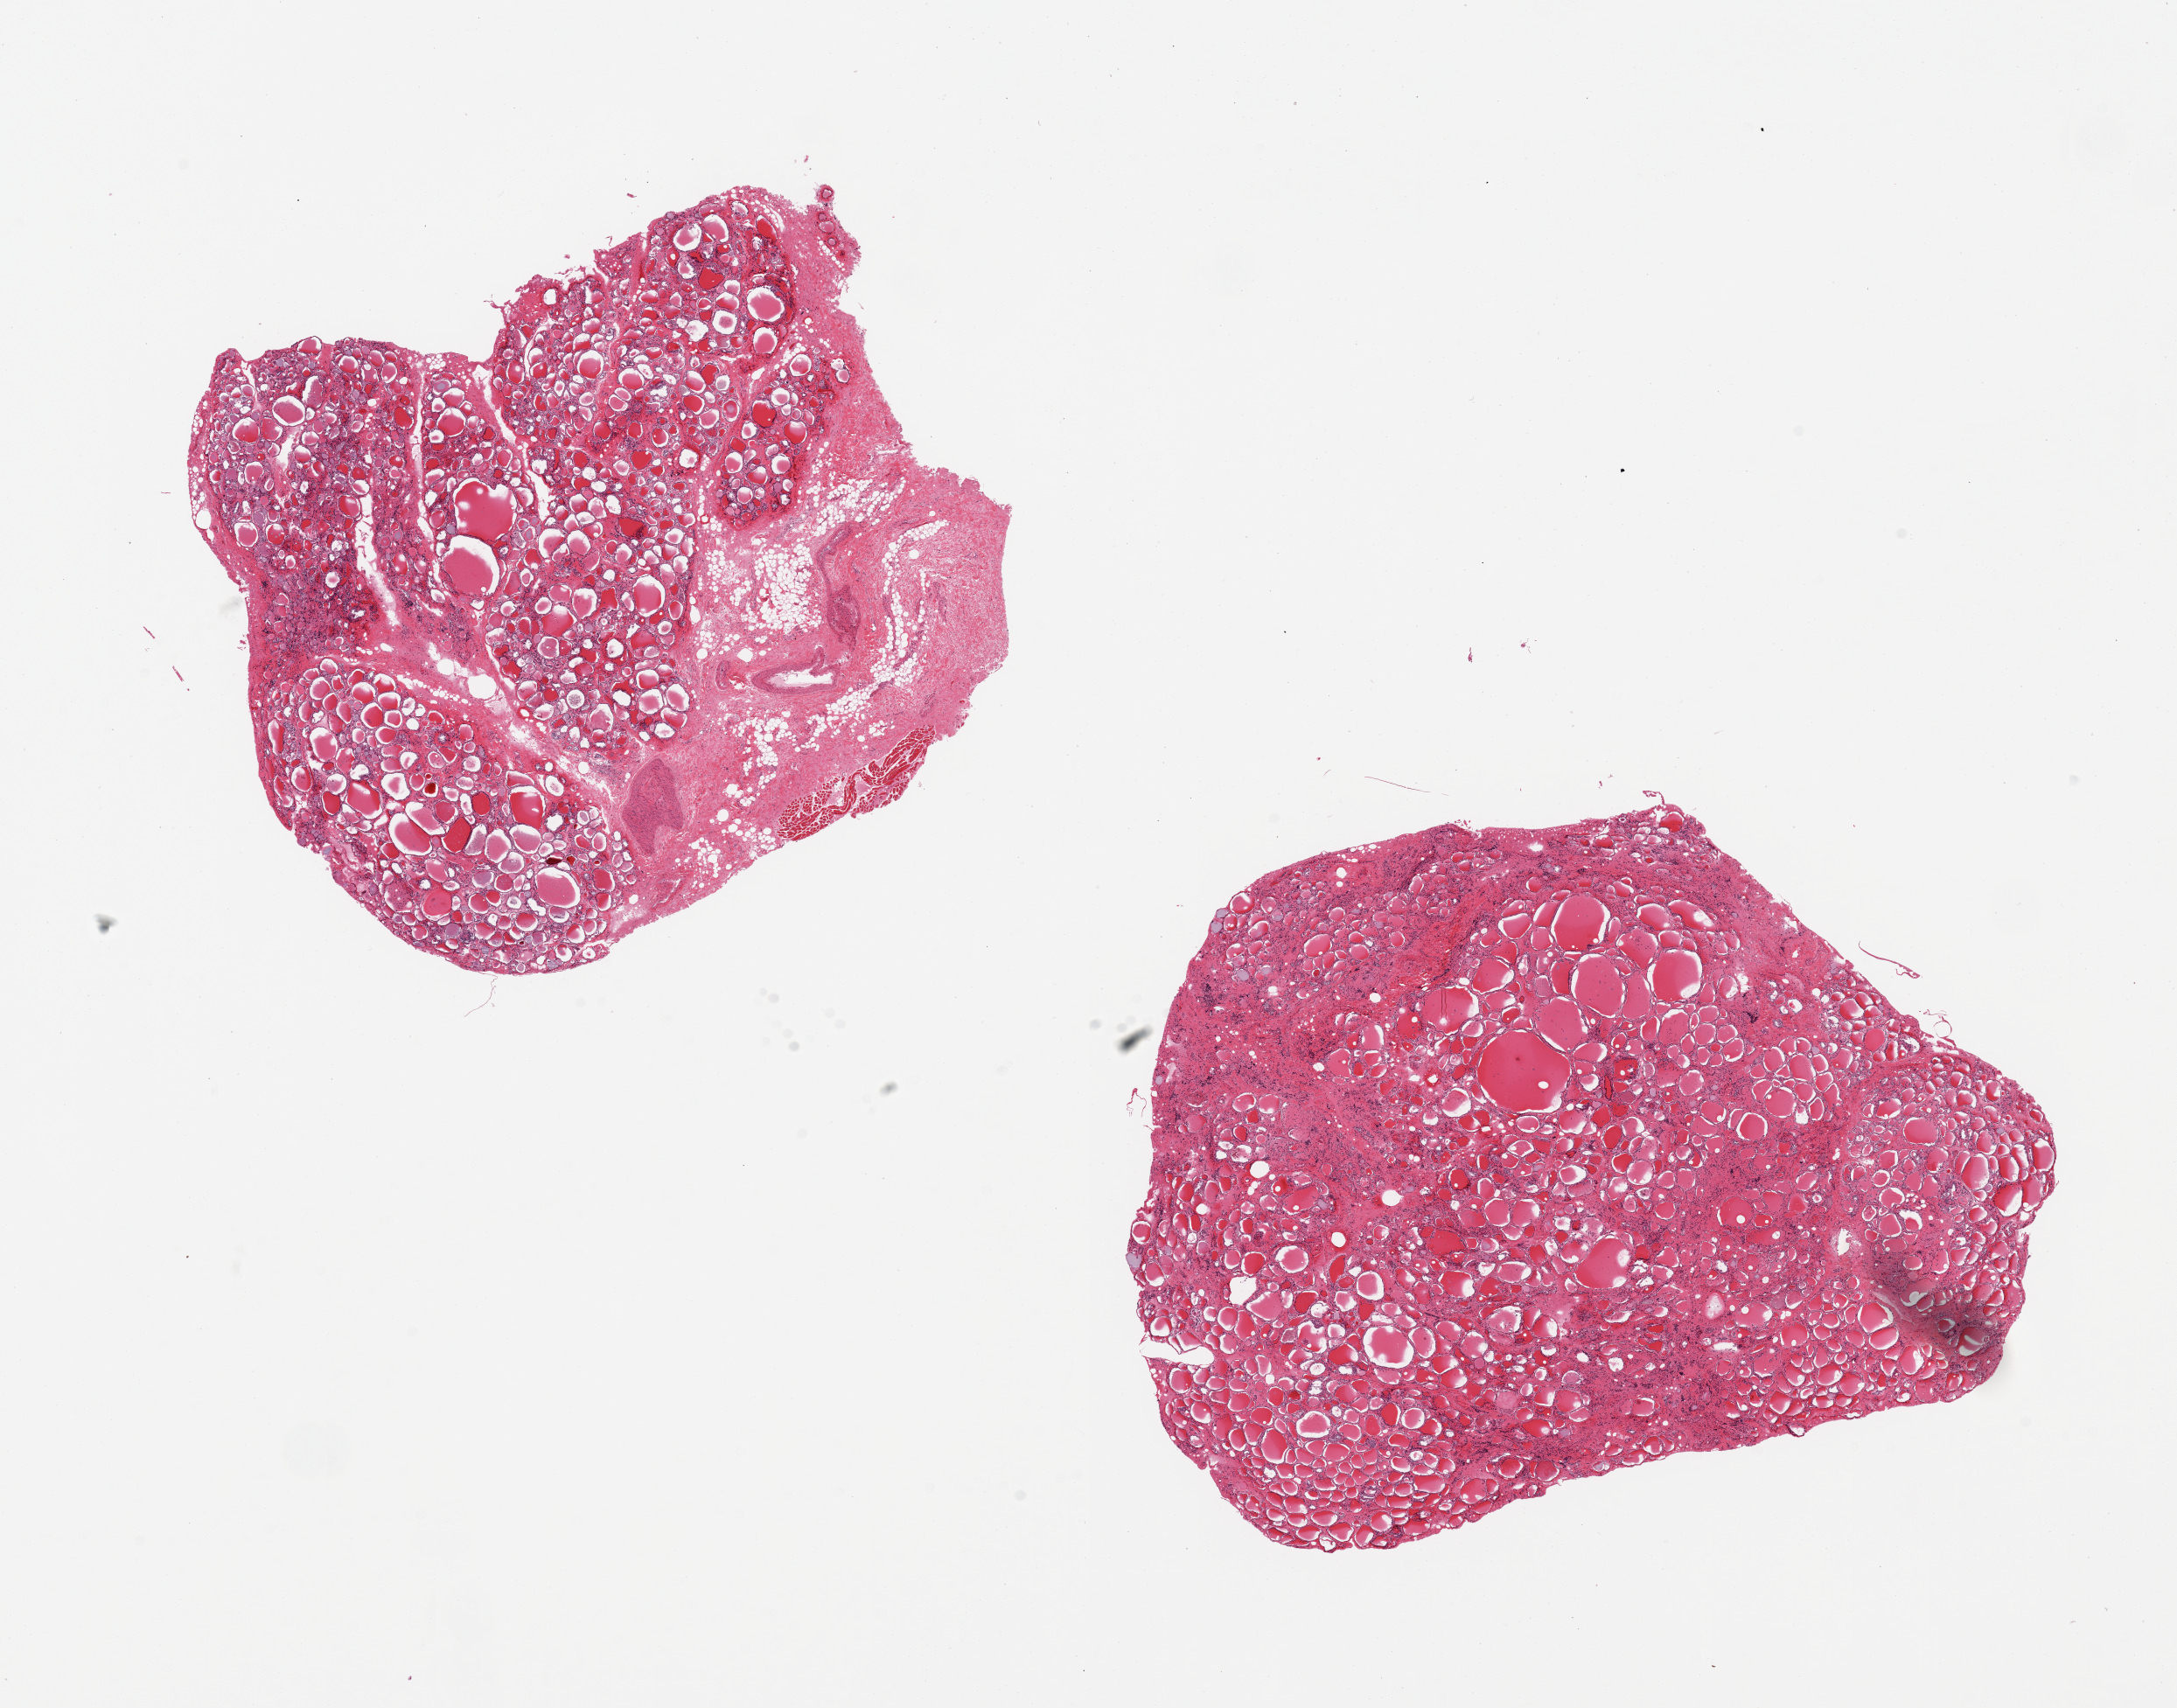
Whole-slide image, hematoxylin and eosin (H&E) stain — a low-resolution overview of the entire scanned area, about 19.7 x 15.4 mm (from a 20x scan); PAXgene-fixed paraffin-embedded (PFPE) section; section of thyroid (target tissue); tissue donor sample. Donor sex: male.
Pathologist's review note for this sample: 2 pieces; one piece with external fibrovascular and skeletal muscle tissue; mild interstitial fibrosis and lymphocytic infiltrate.